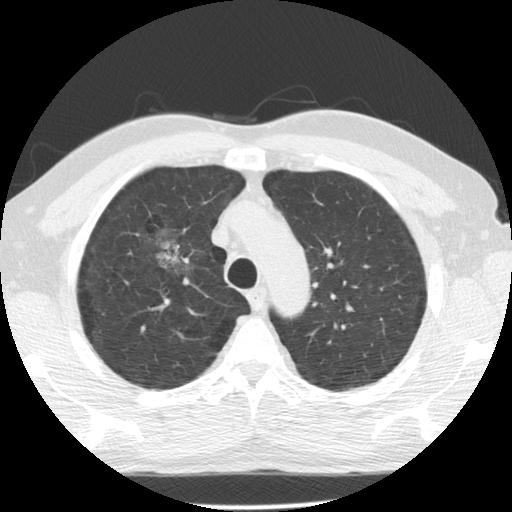
Low-dose screening chest CT, axial slice, second screening round (one year after baseline), lung window (W 1500 / L -600 HU), 140 kVp, slice 99 of 135 in the series, 512 × 512 image matrix. Male participant, aged 60 years at enrolment. Former smoker at enrolment.
Expert-annotated lung lesion, bounding box [x1, y1, x2, y2] px = [133, 219, 195, 279]. The exam's reader record, not a measurement of the box and not confirmed to be the same lesion: non-calcified nodule or mass ≥4 mm, right upper lobe, poorly defined margins, mixed attenuation, pre-existing on the prior screen: yes; interval growth: yes. Official screen result: positive, other. Later outcome: lung cancer diagnosed 562 days after this screen — papillary adenocarcinoma, NOS, right upper lobe, moderately differentiated (G2), stage IB (AJCC 6th edition), 32 mm at pathology.